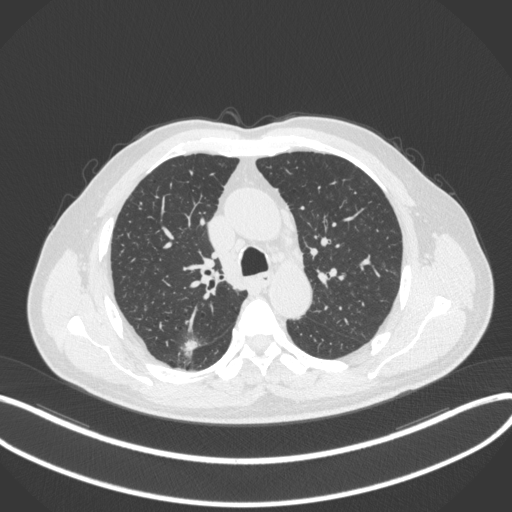
Chest CT, one axial slice. Slice 254 of 366 in the series (ordered by position). Reconstruction kernel B31f. Lung window (W 1500 / L -600 HU). 512 × 512 image matrix, field of view 400 × 400 mm. Male patient, age 69 years. From the clinical record (not read from this slice): clinical TNM (as recorded): T1b N0 M0.
Structures marked on this image (bounding box drawn by a radiologist):
- lung tumour (recorded histology: adenocarcinoma): bounding box (x1, y1, x2, y2) in pixels: (177, 338, 199, 362)